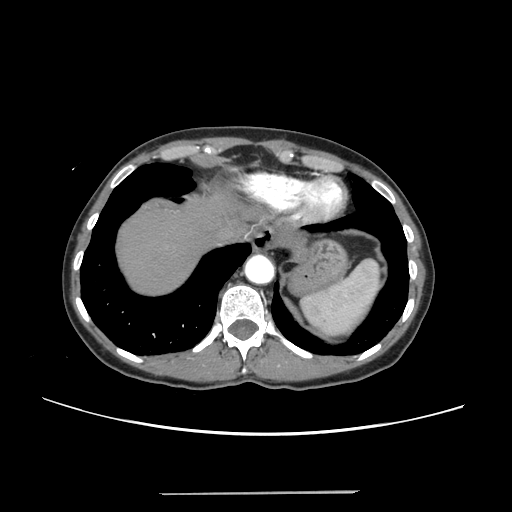
Contrast-enhanced abdominal CT, one axial slice. Position 215 of 240 along the scan axis. 120 kVp. Intravenous contrast given. Soft-tissue window (W 400 / L 40 HU). 512 × 512 image matrix, field of view 371 × 371 mm. Female patient, age 60 years. Case-level facts recorded for this patient, not image findings: diagnosis: colorectal cancer liver metastases, imaged before liver resection; multiple liver metastases: no; largest metastasis: 1.5 cm; disease in both lobes: no.
Outlined on this slice (outlined manually by an expert reader):
- liver: bounding box <117,194,239,294> (left, top, right, bottom; pixels)
- planned liver remnant (the part of the liver to remain after resection): <117,194,239,294>